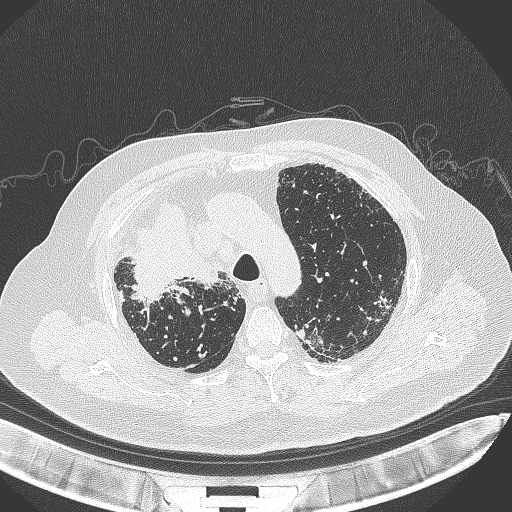
Chest CT, one axial slice. Slice 270 of 384 in the series (ordered by position). 120 kVp. Lung window (W 1500 / L -600 HU). 1 mm slice thickness. 512 × 512 image matrix, field of view 400 × 400 mm. Patient: male, 69 years. From the clinical record (not read from this slice): clinical TNM (as recorded): T4 N3 M1.
Annotated regions visible in this slice (bounding box drawn by a radiologist):
- lung tumour (recorded histology: adenocarcinoma): box from (x=119, y=203) to (x=224, y=303) px